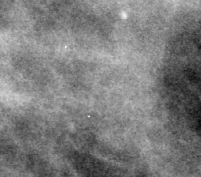
Cropped region of a digitized screen-film mammogram centred on a radiologist-marked abnormality, left breast, MLO view.
Finding: calcifications, morphology punctate; BI-RADS assessment category 2; benign; no additional work-up was recommended (benign without callback).